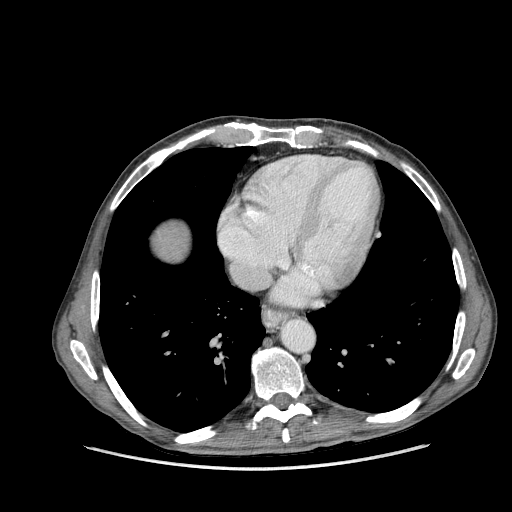
Contrast-enhanced abdominal CT (liver protocol), one axial slice; slice 147 of 162 in the series (ordered by position); reconstruction kernel STANDARD; soft-tissue window (W 400 / L 40 HU); 2.5 mm slice thickness; 512 × 512 image matrix, field of view 400 × 400 mm. Case-level facts recorded for this patient, not image findings: diagnosis: hepatocellular carcinoma (patient treated with transarterial chemoembolisation; whether this scan precedes or follows treatment is not stated here); TNM stage (as recorded): Stage-IIIA; Child-Pugh class: A.
Annotated regions visible in this slice (semi-automatically segmented with operator editing):
- liver parenchyma outside the tumour (the mass and vessels are separate outlines, so this box may not span the whole liver): bounding box [x1, y1, x2, y2] px = [154, 222, 188, 260]